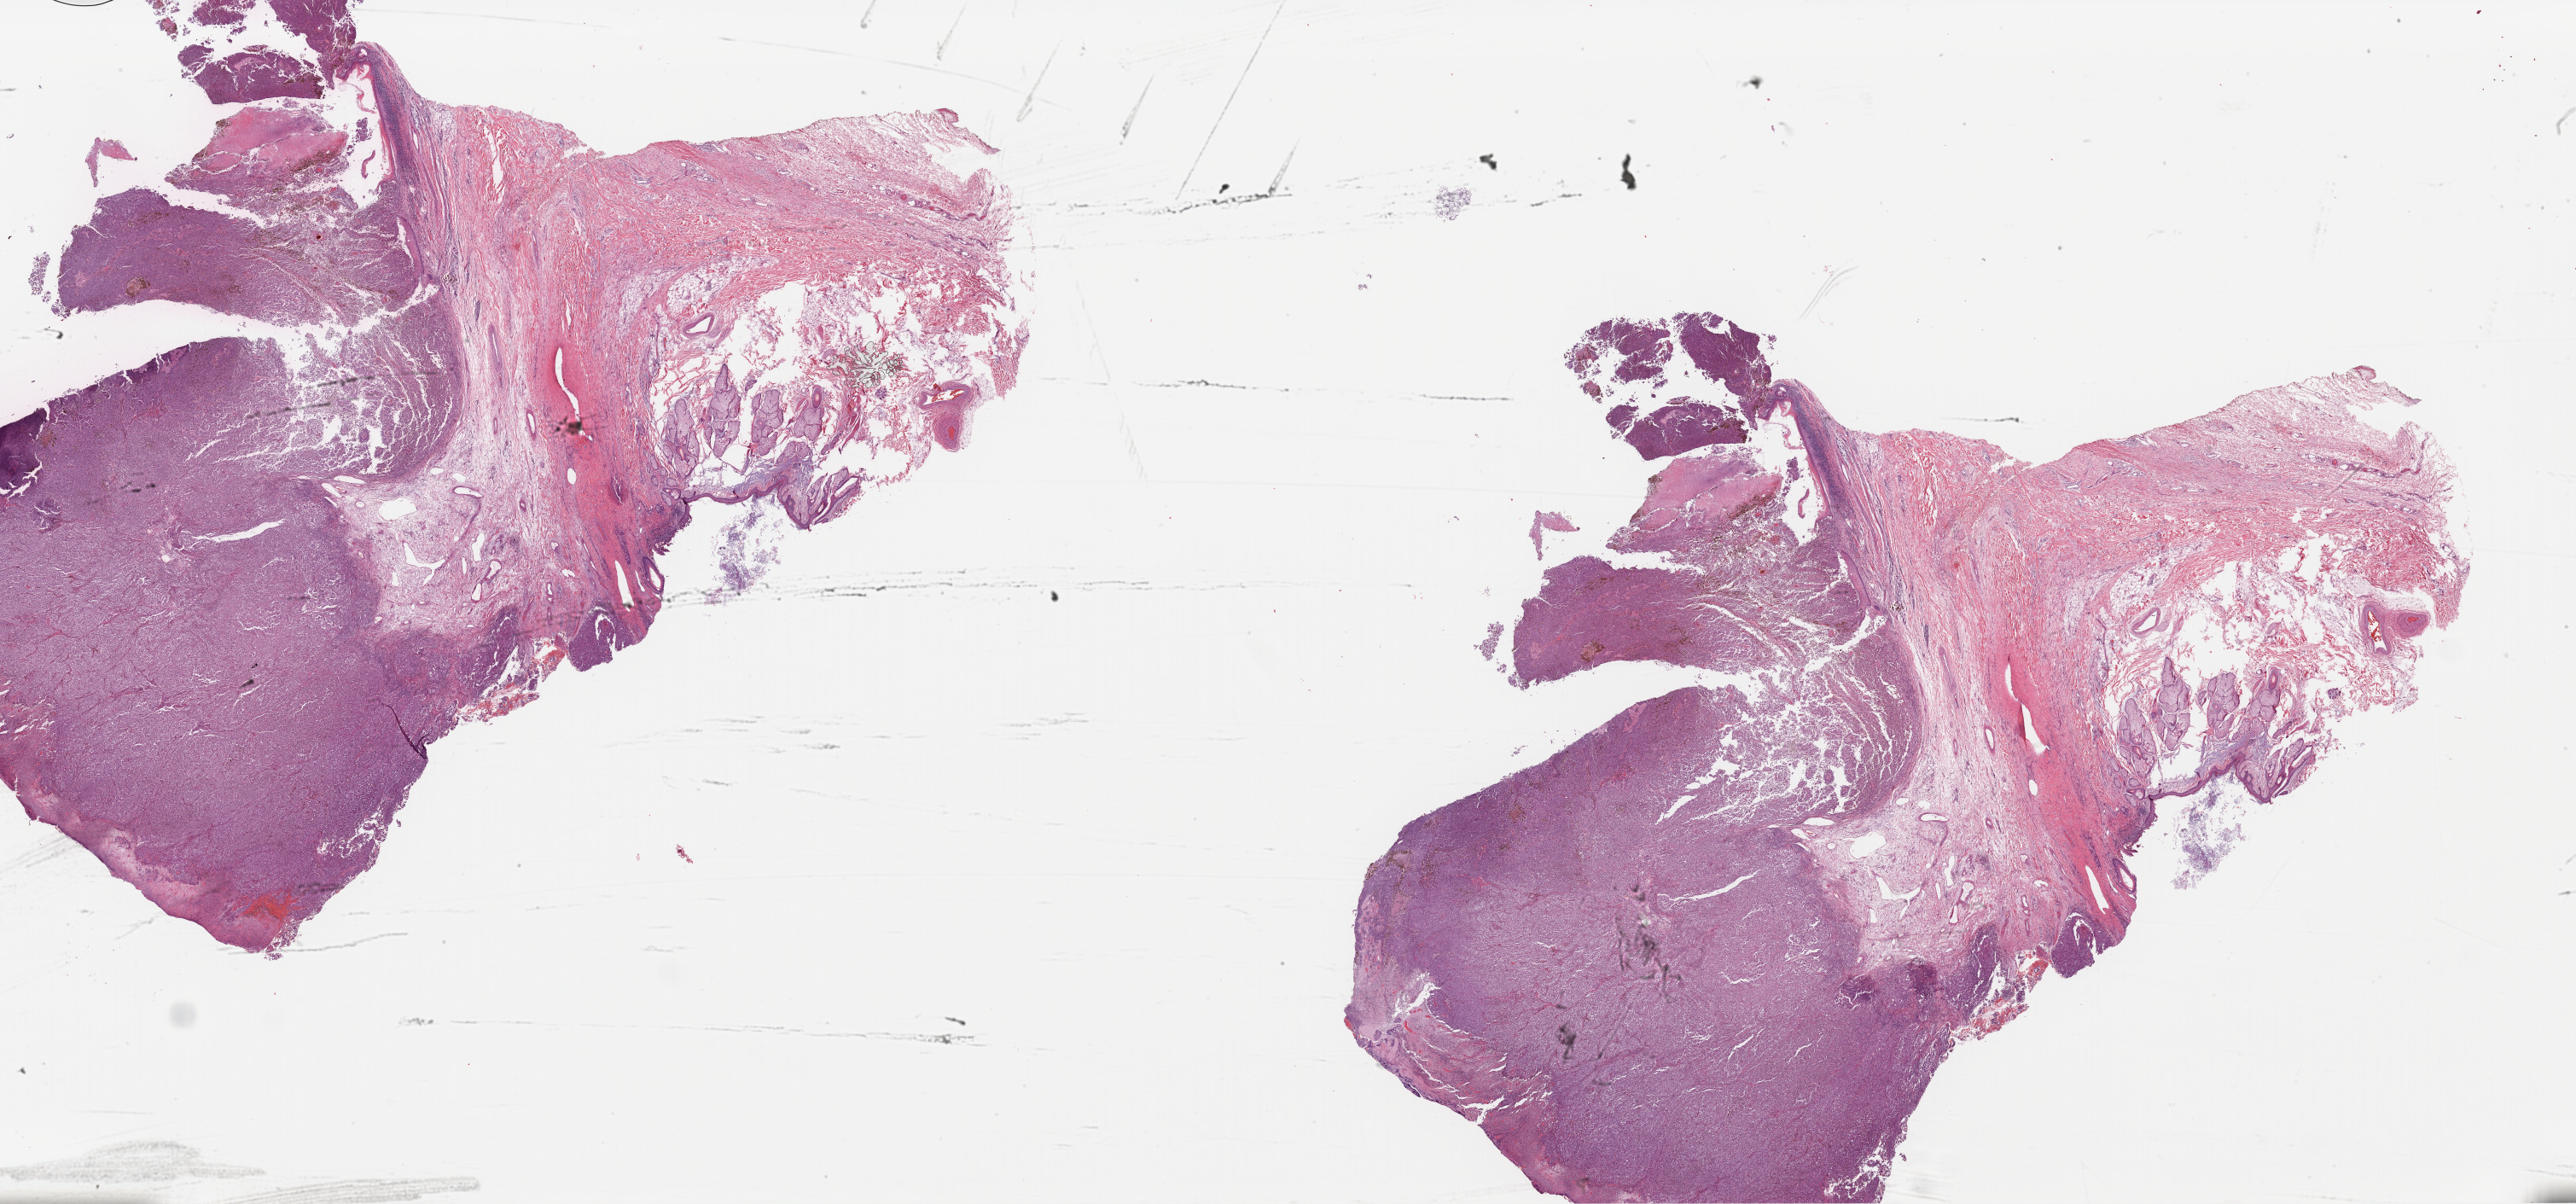
Whole-slide histology image, Hematoxylin and eosin (H&E) stained, whole scanned area (about 47.7 x 22.3 mm, acquisition: 40x scan) shown as a low-resolution overview. Formalin-fixed paraffin-embedded (FFPE) diagnostic section. Sample: primary tumour, skin. Male patient; age at initial diagnosis 61 years.
* histologic diagnosis: Nodular melanoma